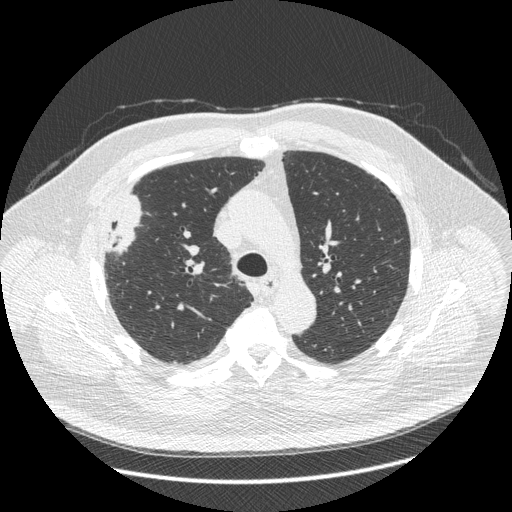
Low-dose screening chest CT, one axial slice; position 299 of 426 along the scan axis; reconstruction kernel STANDARD; 120 kVp; lung window (W 1500 / L -600 HU); 1.25 mm slice thickness; 512 × 512 image matrix, field of view 400 × 400 mm.
Structures marked on this image (expert manual segmentation):
- lesion 1 (tumor, upper lobe of right lung): bounding box <104,195,142,253> (left, top, right, bottom; pixels)